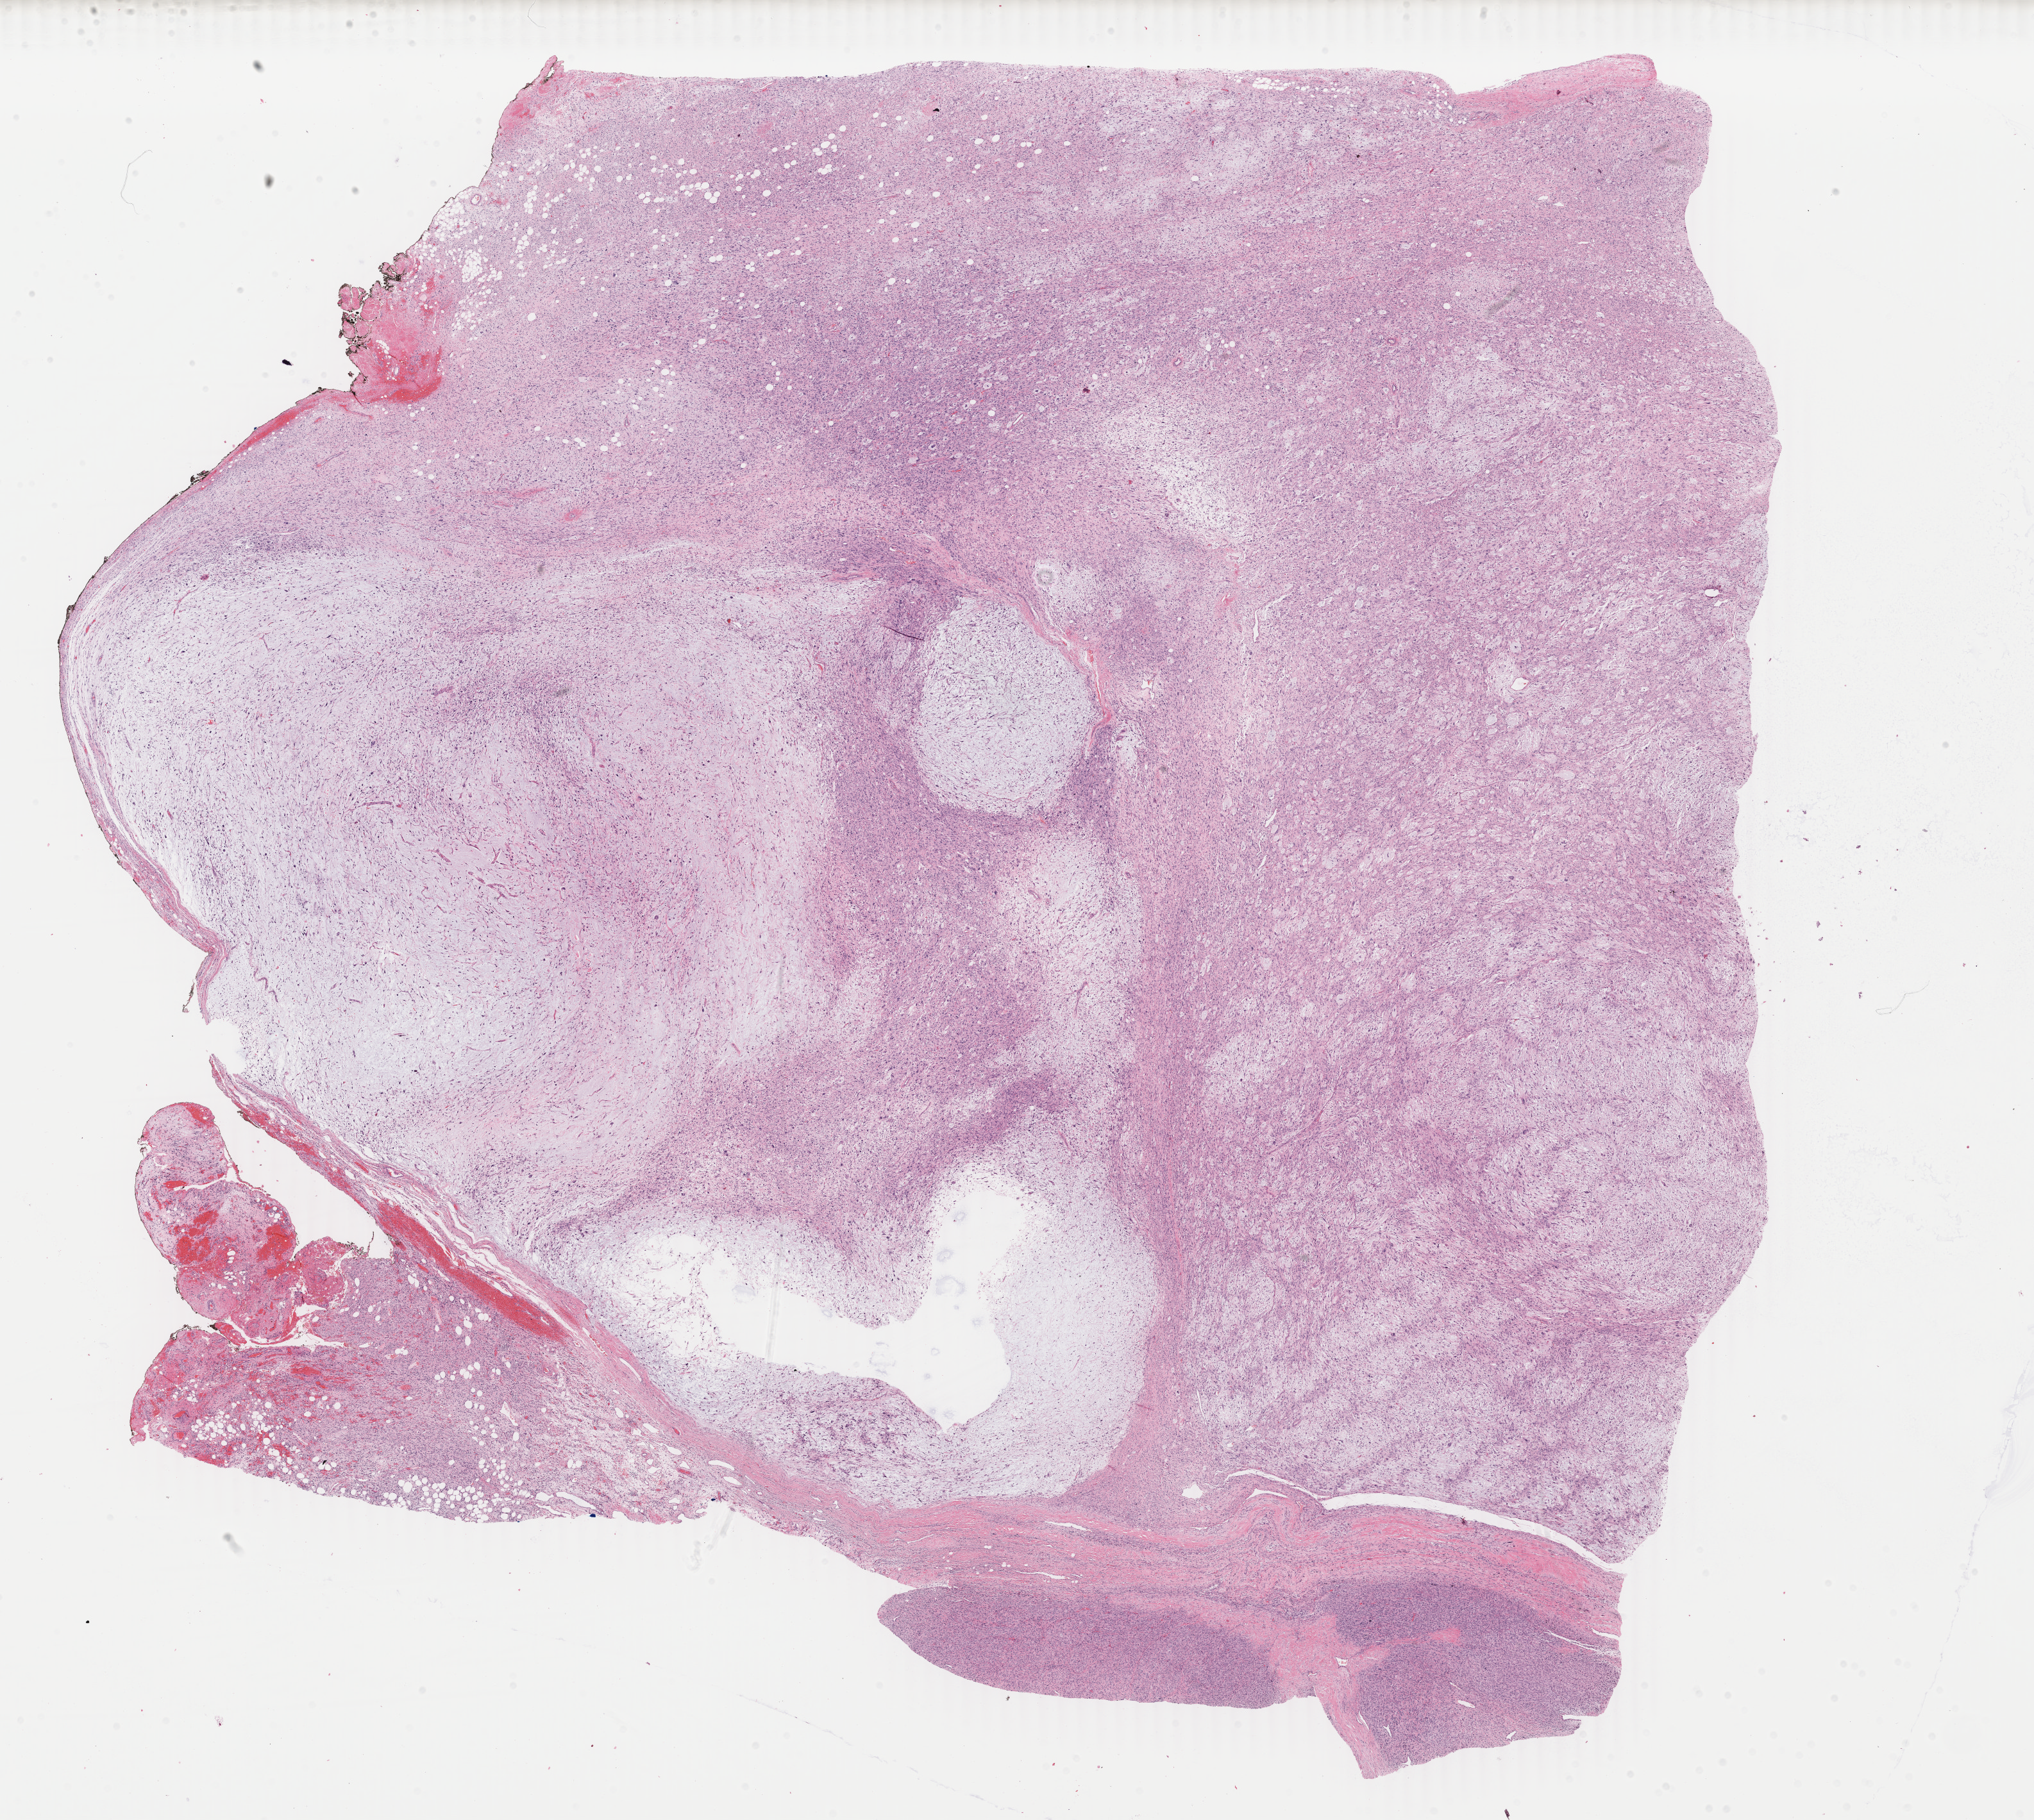
Digitized Hematoxylin and eosin (H&E) stained tissue section (whole slide), a low-resolution overview of the entire scanned area, about 25.2 x 22.6 mm. Formalin-fixed paraffin-embedded (FFPE) diagnostic section. Connective, subcutaneous and other soft tissues, primary tumour sample. Male patient; age at initial diagnosis 55 years.
Diagnosis: Fibromyxosarcoma (connective, subcutaneous and other soft tissues of lower limb and hip).